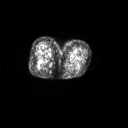
FDG PET of an extremity soft-tissue mass (from a PET/CT study), one axial slice. Position 21 of 267 along the scan axis. 3.27 mm slice thickness. 128 × 128 image matrix, field of view 700 × 700 mm. Patient: female, 70 years. Case-level facts recorded for this patient, not image findings: histological type: synovial sarcoma; grade: intermediate; site of the primary tumour: right buttock.
Annotated regions visible in this slice (expert contour drawn on MRI and transferred to this co-registered scan by the dataset authors):
- gross tumour volume including surrounding oedema: bounding box [x1, y1, x2, y2] px = [35, 62, 39, 68]